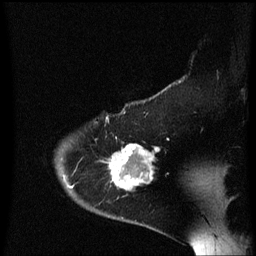
Breast MRI (dynamic contrast-enhanced), one sagittal slice. Slice 49 of 60 in the series (ordered by position). Dynamic contrast-enhanced series, image 2 of 3 at this slice position (ordered by acquisition). 1.5 T. TE 4.2 ms, TR 8.4 ms. 2 mm slice thickness. 256 × 256 image matrix. Patient: female, 54 years. Case-level facts recorded for this patient, not image findings: setting: breast cancer imaged before/during neoadjuvant chemotherapy; receptor status: HR-positive, HER2-negative.
Structures marked on this image (semi-automatic segmentation, software-assisted and operator-edited):
- analysis volume of interest (the breast-tissue region the enhancement analysis was run in; not a lesion): bounding box (x1, y1, x2, y2) in pixels: (106, 132, 162, 199)
- tumour enhancement mask (voxels above the 70 % enhancement threshold inside the analysis volume of interest): (109, 144, 160, 189)